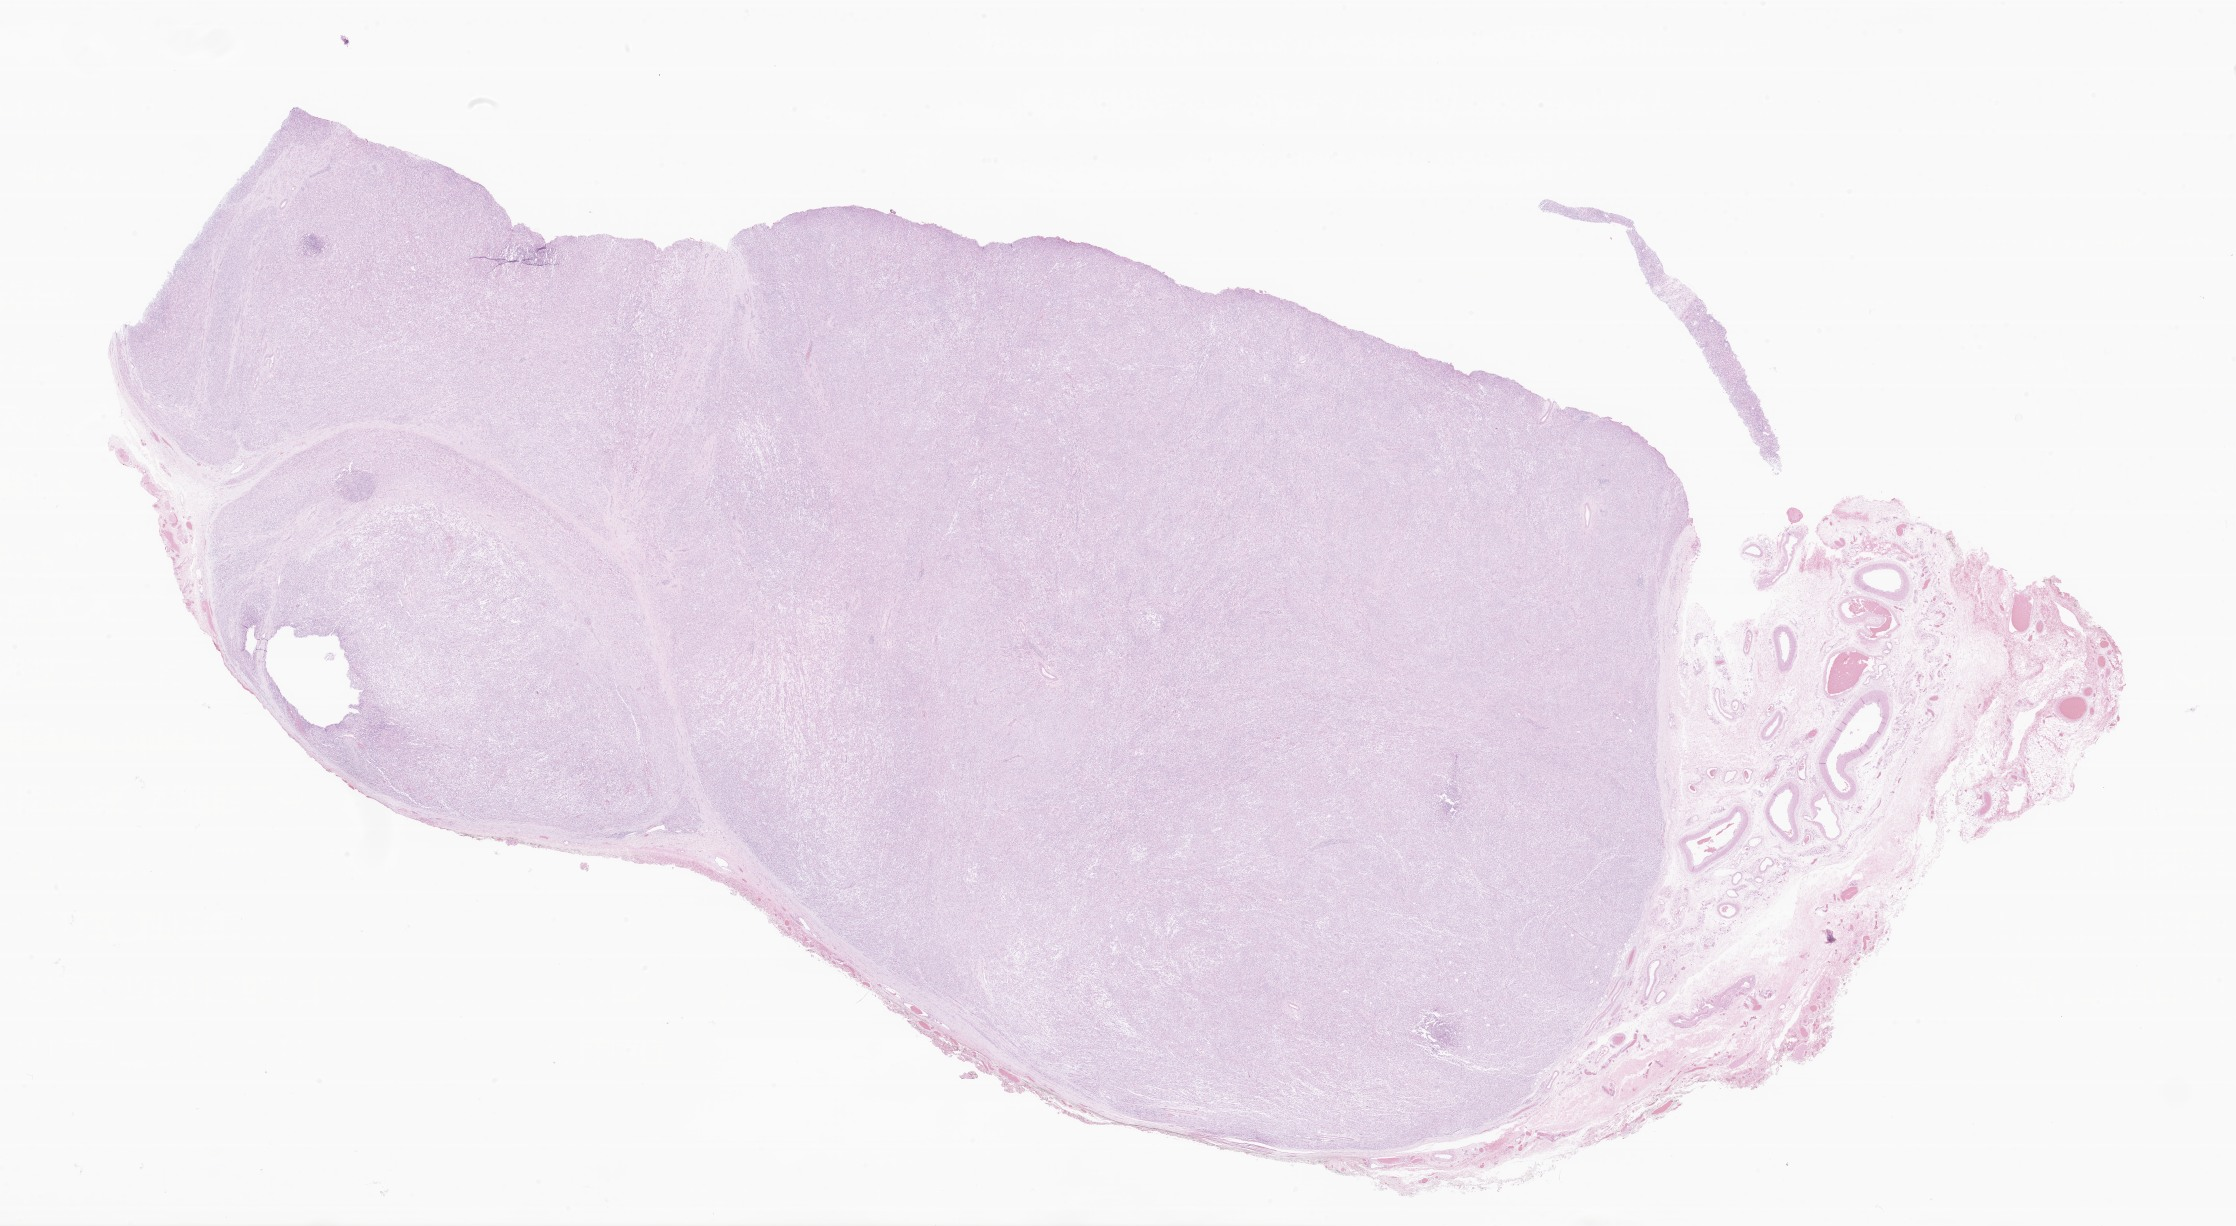
Digitized H&E-stained section of tumor tissue from the scrotum, low-resolution overview of the scanned area, about 37.7 x 20.7 mm, formalin-fixed, paraffin-embedded (FFPE) tissue. Patient: male, age 196 months.
* diagnosis: Embryonal rhabdomyosarcoma, NOS